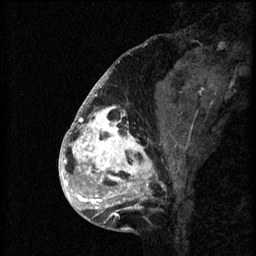
Breast MRI (dynamic contrast-enhanced), one sagittal slice; slice 23 of 60 in the series (ordered by position); 3 images stored at this slice position (order not interpretable as contrast timing); 1.5 T; TE 4.2 ms, TR 8.2 ms; 2 mm slice thickness; 256 × 256 image matrix, field of view 180 × 180 mm. Patient: female, 41 years.
Structures marked on this image (semi-automatic segmentation, software-assisted and operator-edited):
- analysis volume of interest (the breast-tissue region the enhancement analysis was run in; not a lesion): box from (x=72, y=108) to (x=175, y=205) px
- tumour enhancement mask (voxels above the 70 % enhancement threshold inside the analysis volume of interest): (x=72, y=108)–(x=164, y=205)